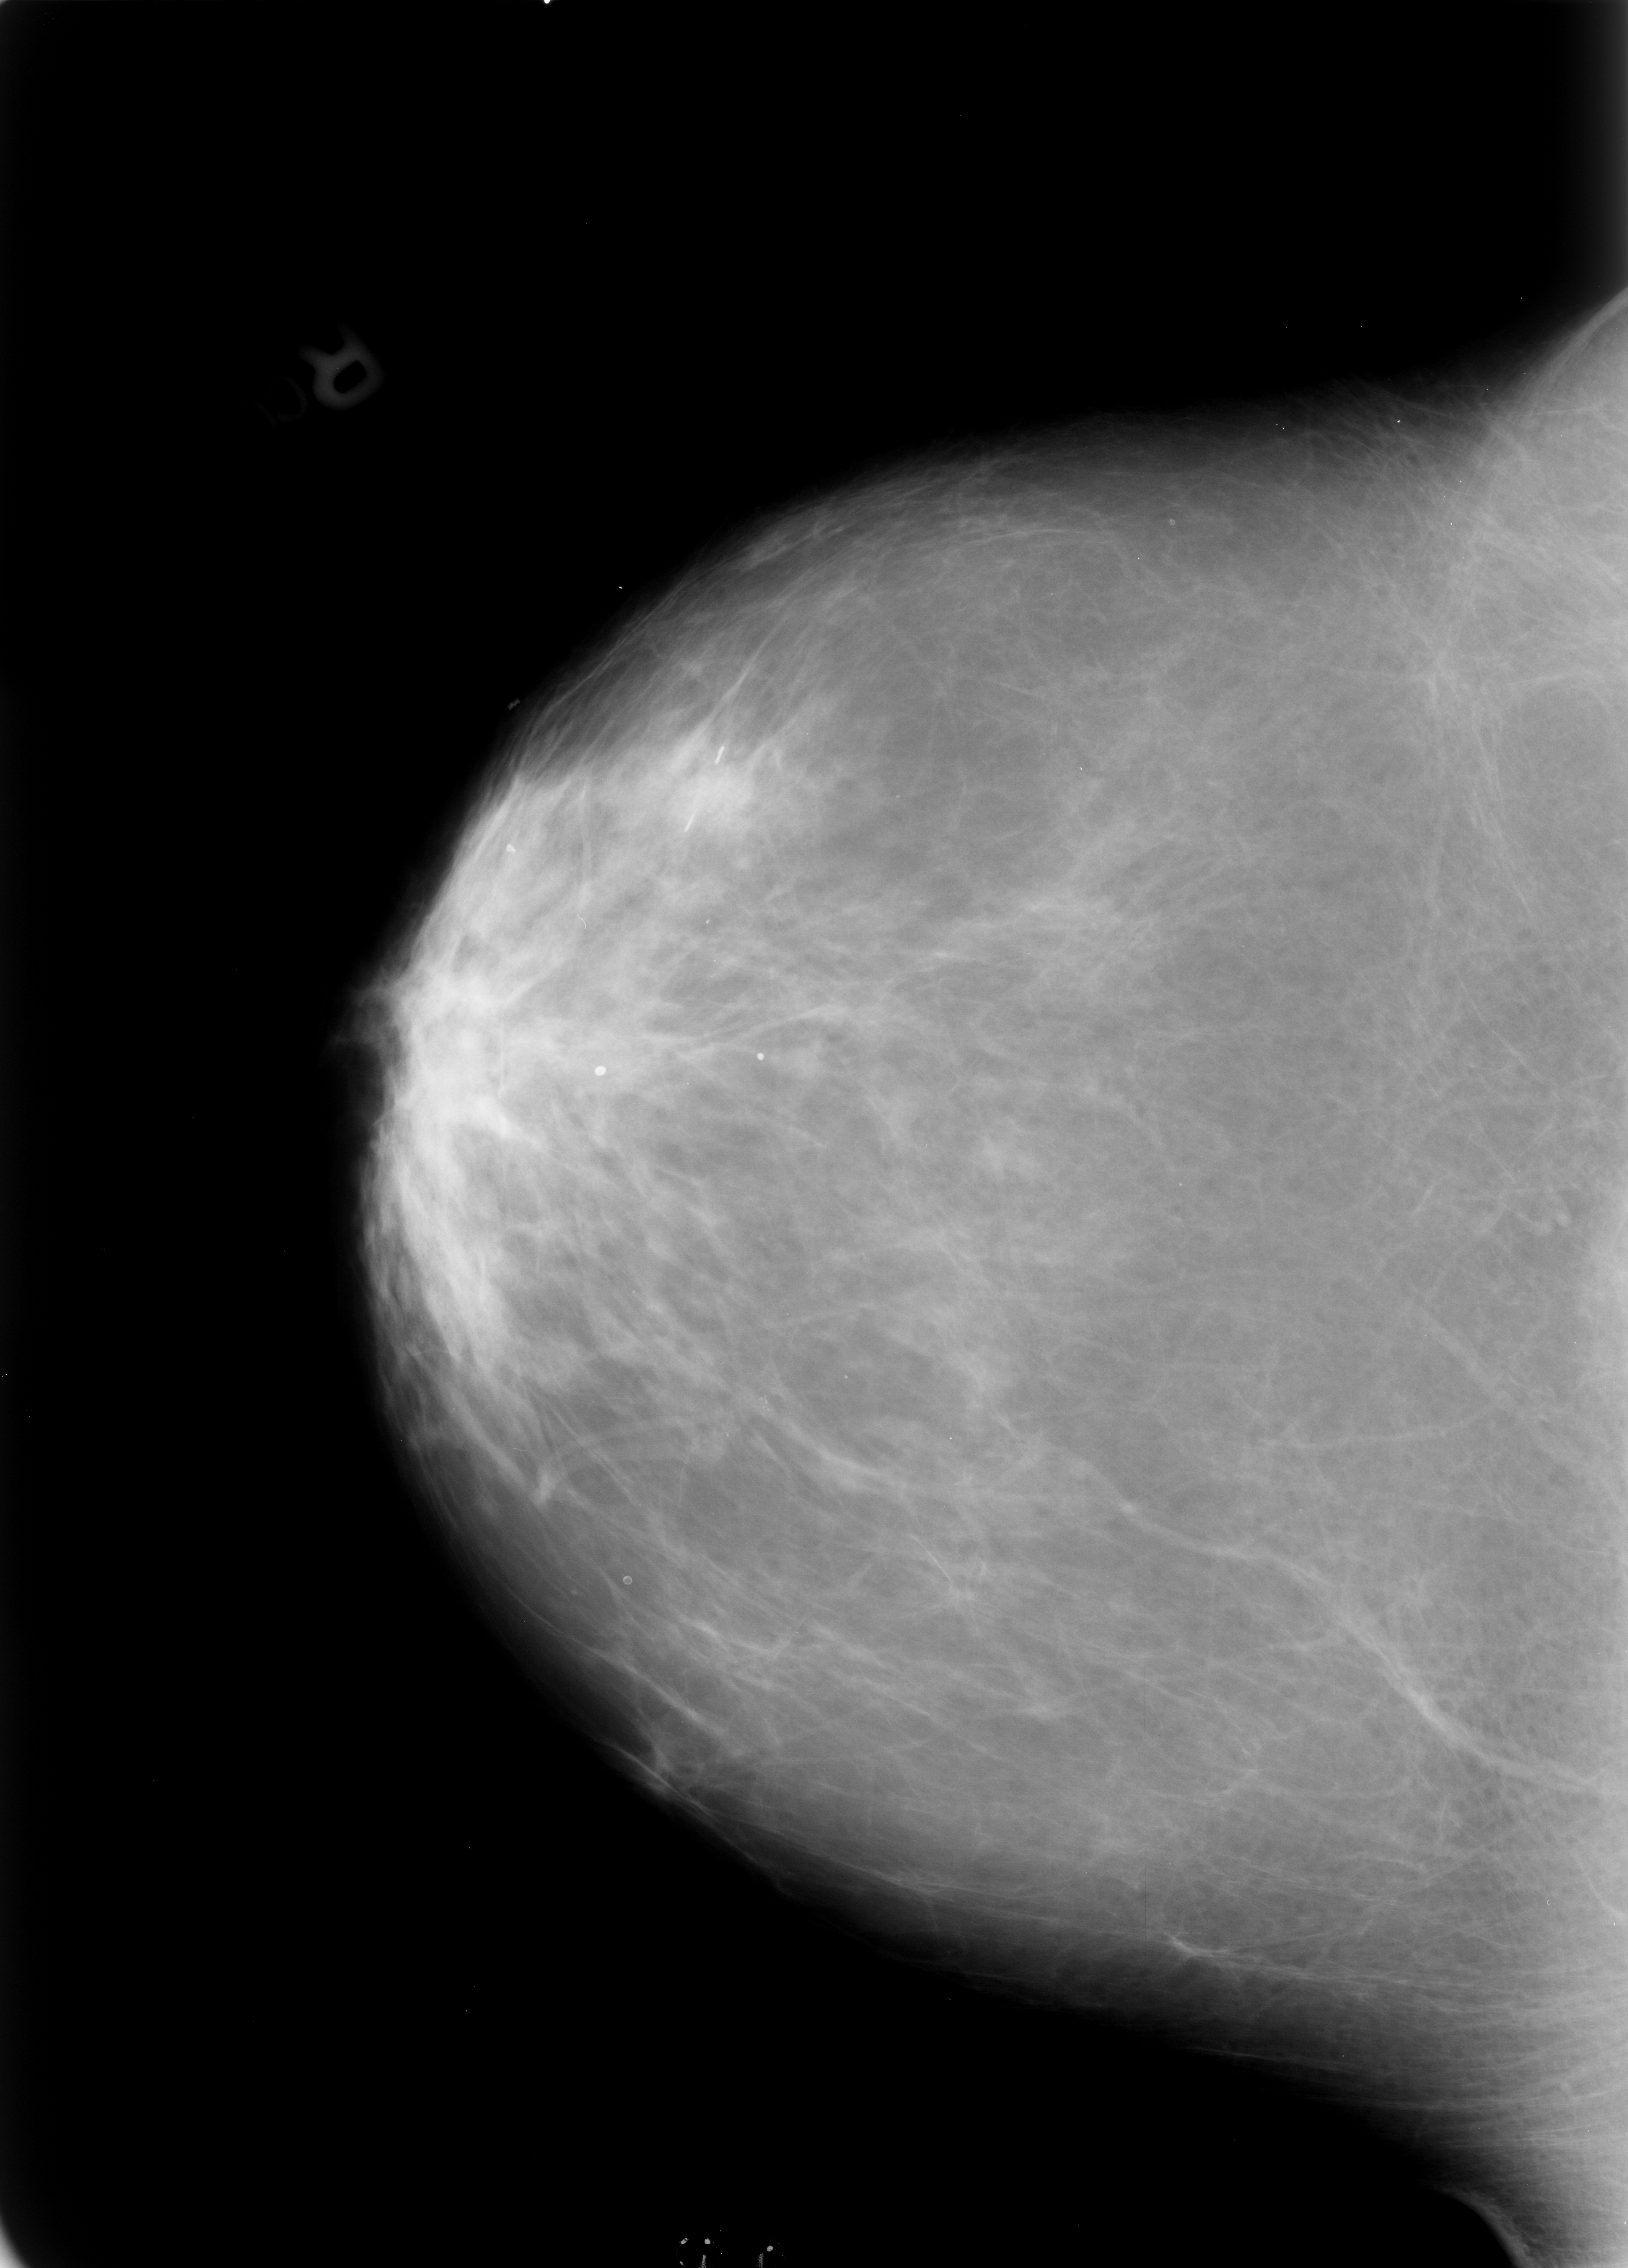
Digitized screen-film mammogram. Right breast. Craniocaudal (CC) view. 1628 × 2268 image matrix.
Expert-marked regions of interest on this image (one box per marked abnormality):
- calcifications, morphology pleomorphic, distribution clustered; BI-RADS assessment category 4; subtlety rating 2 on a 1 (subtle) to 5 (obvious) scale; pathology result (as recorded, not read from the image): benign: bounding box <704,1360,804,1447> (left, top, right, bottom; pixels)